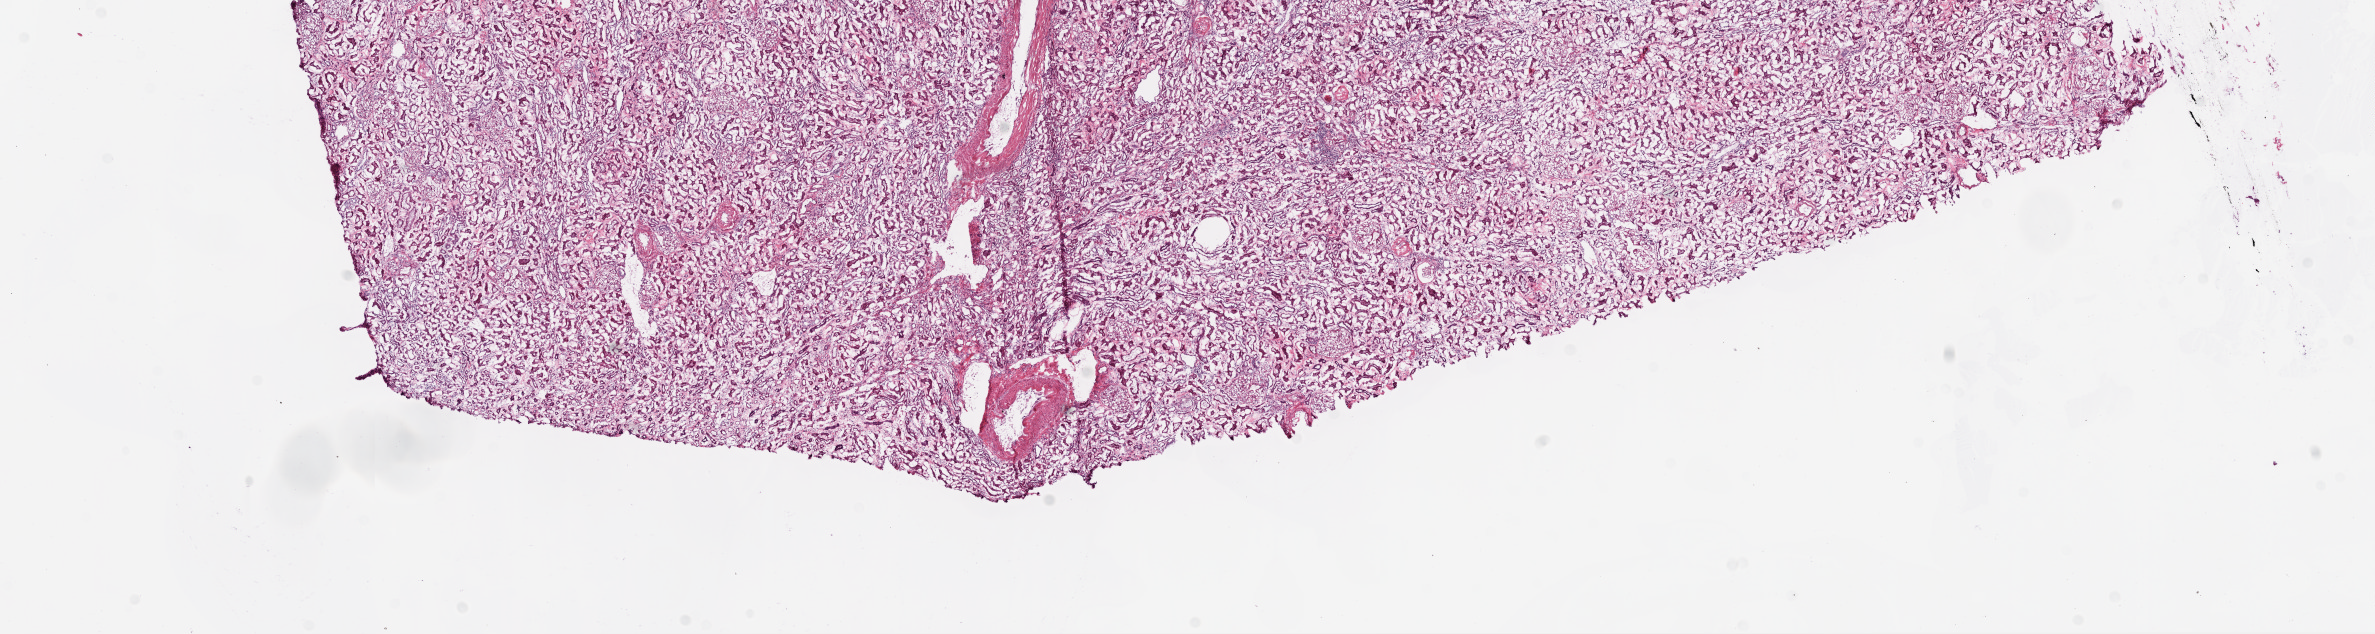
Digitized Hematoxylin and eosin (H&E) stained tissue section (whole slide) — shown as a low-resolution overview of the whole scanned area (about 19.1 x 5.1 mm). Frozen section from the top of the tissue portion. Kidney, solid tissue normal (non-tumour tissue) sample. Female patient; age at initial diagnosis 77 years.
This section: solid tissue normal (non-tumour) sample from the same patient. Patient diagnosis: Clear cell adenocarcinoma, NOS.